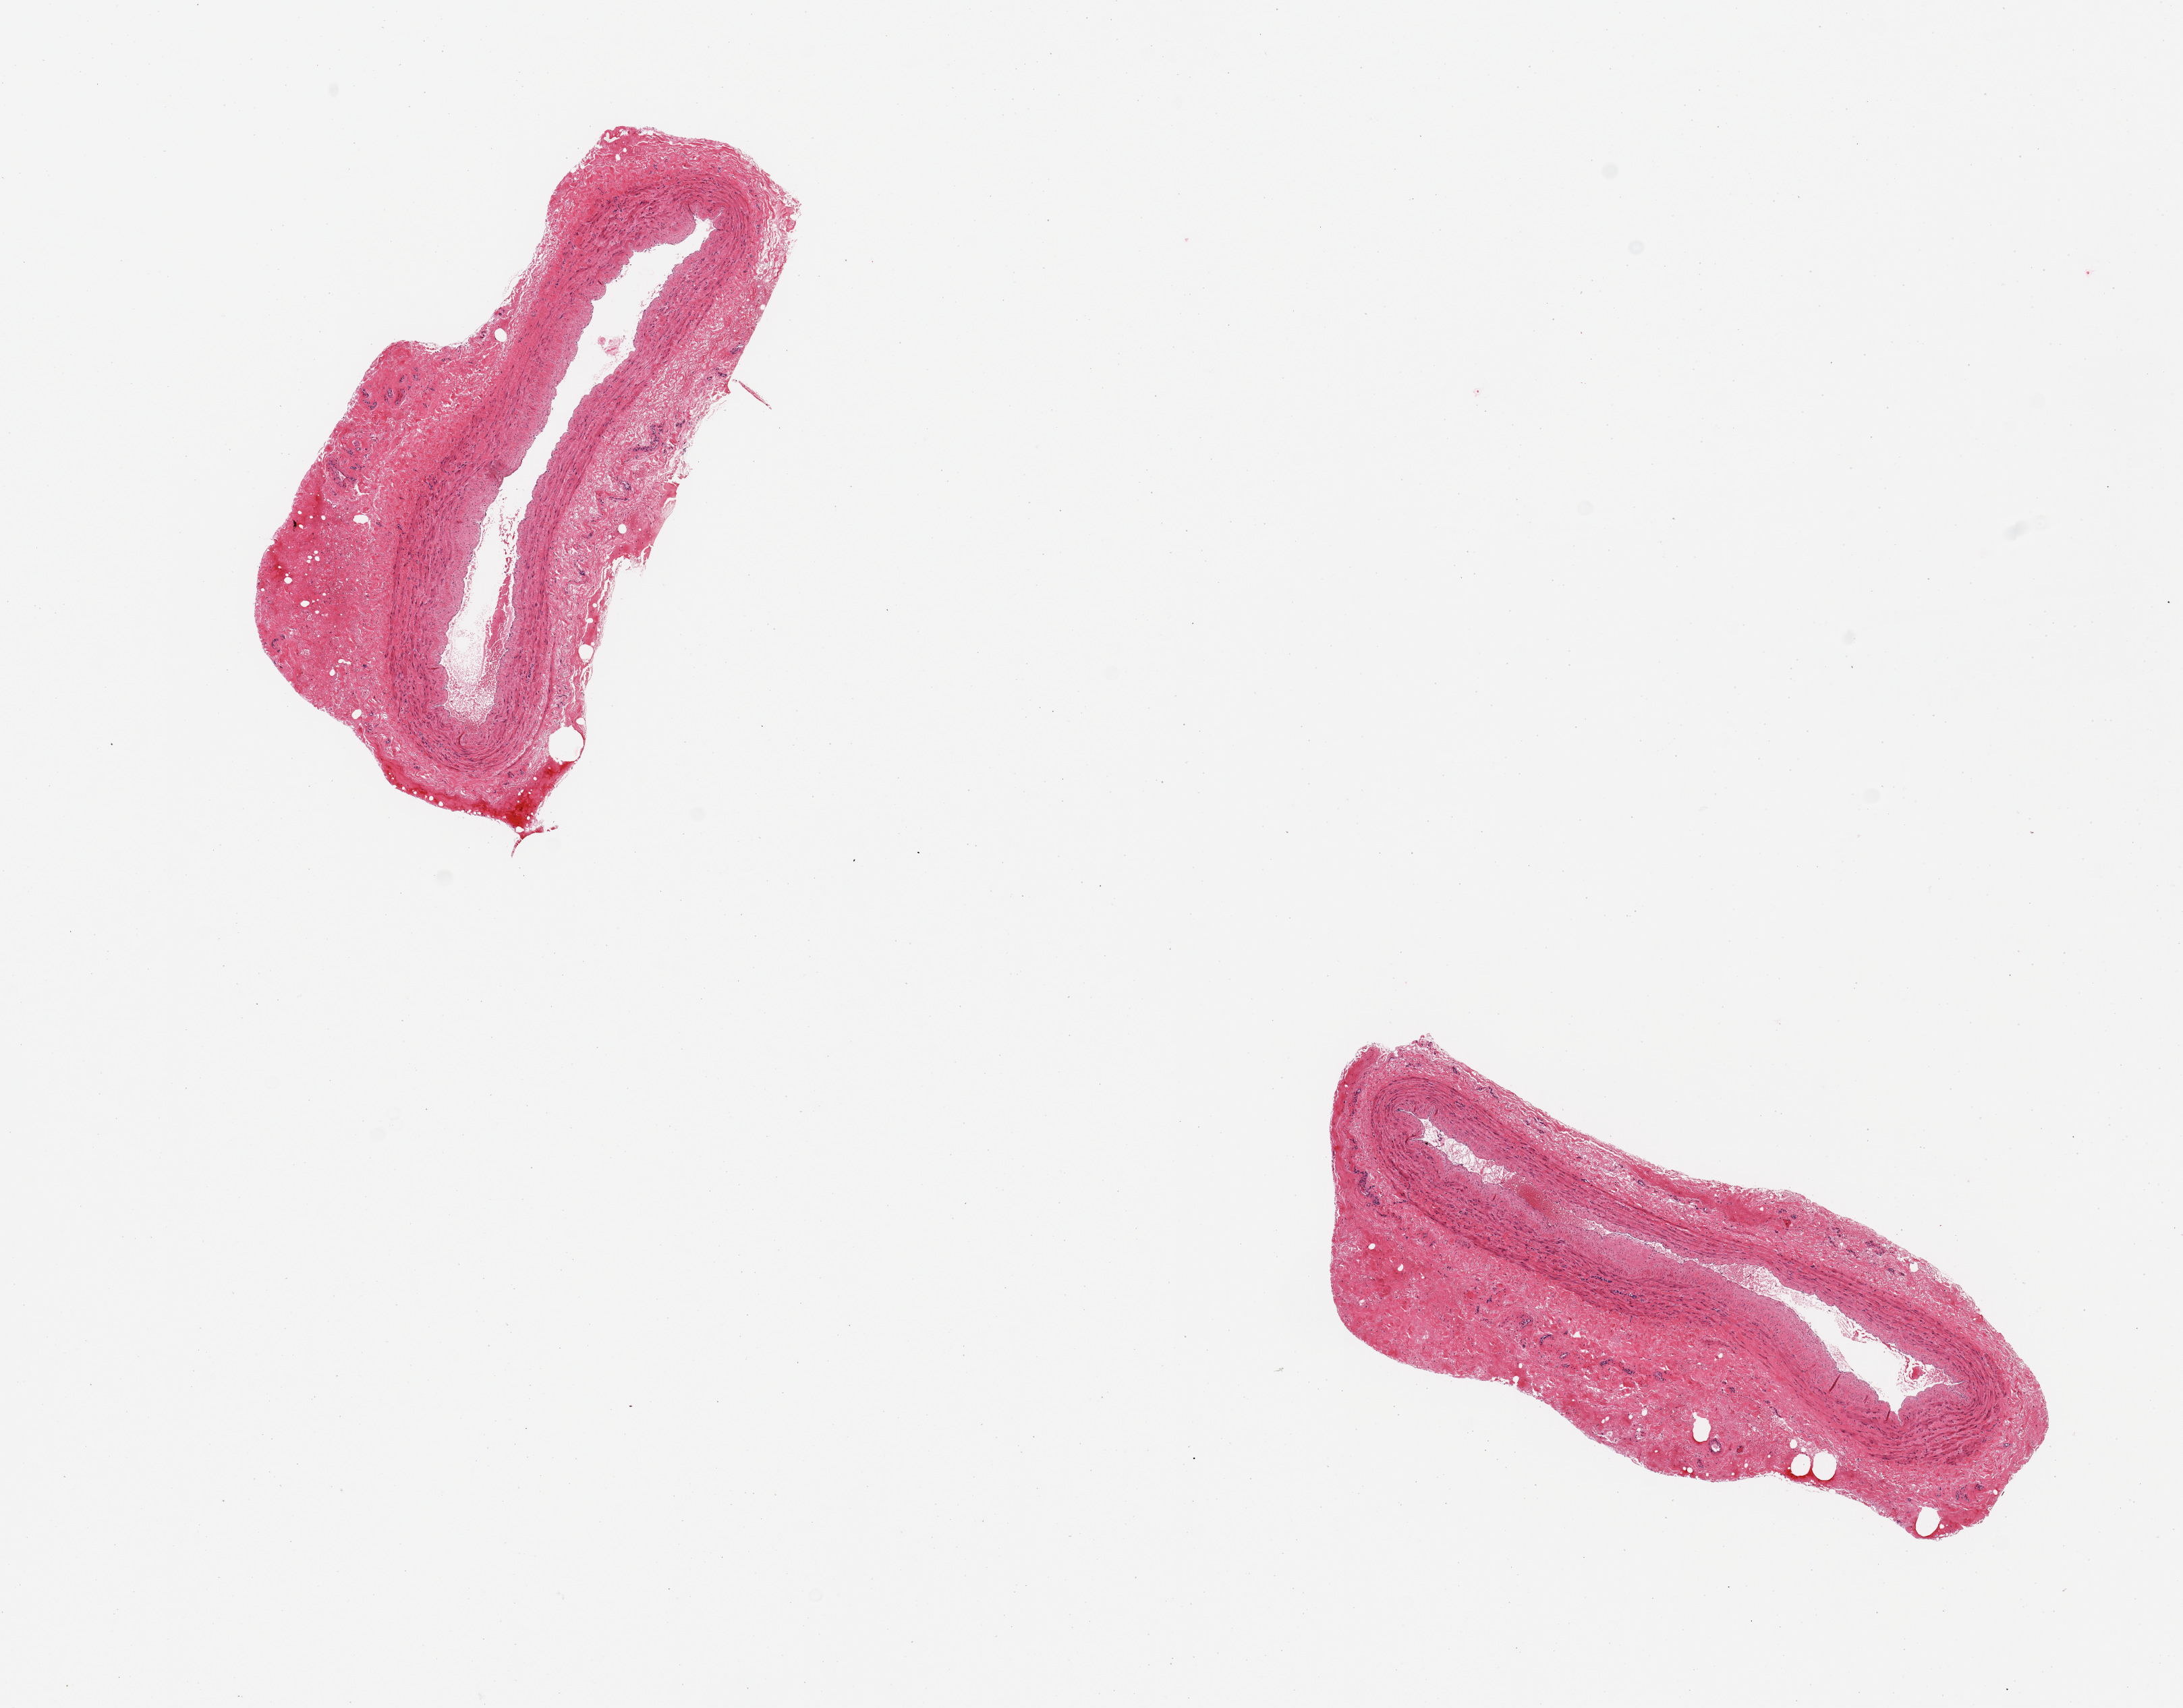
Hematoxylin and eosin (H&E) whole-slide image — whole scanned area (about 12.8 x 10.0 mm, slide scanned at 20x) shown as a low-resolution overview; PAXgene-fixed paraffin-embedded (PFPE) section; target tissue: tibial artery; donor tissue sample. Male donor.
Review note (as recorded): 2 pieces: adventitia measures up to 0.8mm.